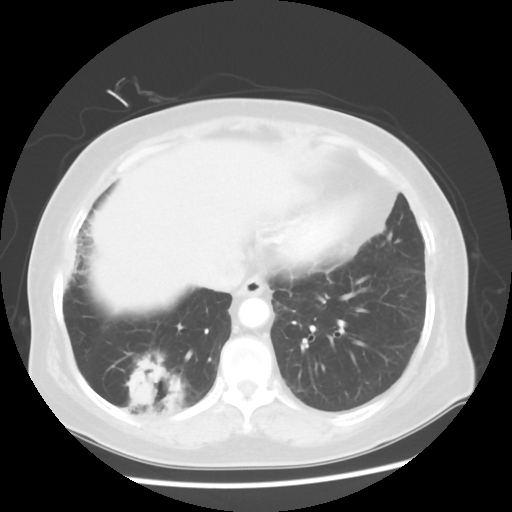
Chest CT, one axial slice. Slice 16 of 56 in the series (ordered by position). Reconstruction kernel STANDARD. 120 kVp. Lung window (W 1500 / L -600 HU). 5 mm slice thickness. 512 × 512 image matrix, field of view 360 × 360 mm. Female patient, age 64 years. Case-level facts recorded for this patient, not image findings: clinical TNM (as recorded): Tis N0 M0.
Structures marked on this image (bounding box drawn by a radiologist):
- lung tumour (recorded histology: adenocarcinoma): bounding box (x1, y1, x2, y2) in pixels: (122, 345, 193, 438)